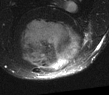
MRI of an extremity soft-tissue mass, one axial slice; slice 32 of 52 in the series (ordered by position); T2-weighted fat-saturated; MR volume resampled by the dataset authors to the PET/CT grid (not the native acquisition matrix); 109 × 95 image matrix, field of view 106 × 93 mm. Male patient. Case-level facts recorded for this patient, not image findings: histological type: synovial sarcoma; site of the primary tumour: left poplietal fossa.
Annotated regions visible in this slice (expert contour drawn on MRI and transferred to this co-registered scan by the dataset authors):
- gross tumour volume (mass): bounding box [x1, y1, x2, y2] px = [19, 19, 77, 71]